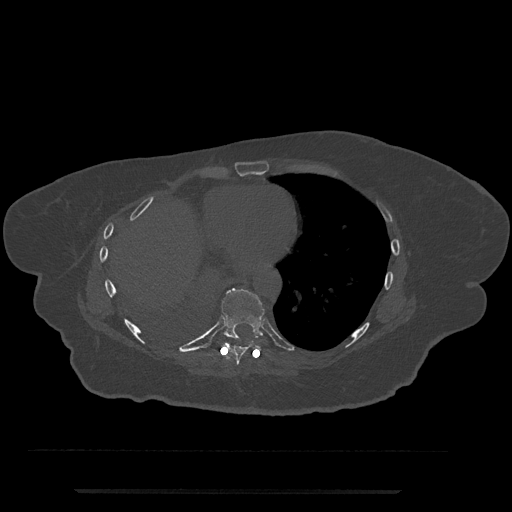
CT including the spine, one axial slice; slice 362 of 797 in the series (ordered by position); 120 kVp; bone window (W 1800 / L 400 HU); 0.5 mm slice thickness; 512 × 512 image matrix, field of view 440 × 440 mm. Patient: female, 51 years. Case-level facts recorded for this patient, not image findings: primary cancer: neuro.
Outlined on this slice (semi-automatic segmentation, software-assisted and operator-edited):
- T8 vertebra: bounding box [x1, y1, x2, y2] px = [229, 343, 248, 365]
- T9 vertebra: [217, 288, 265, 341]